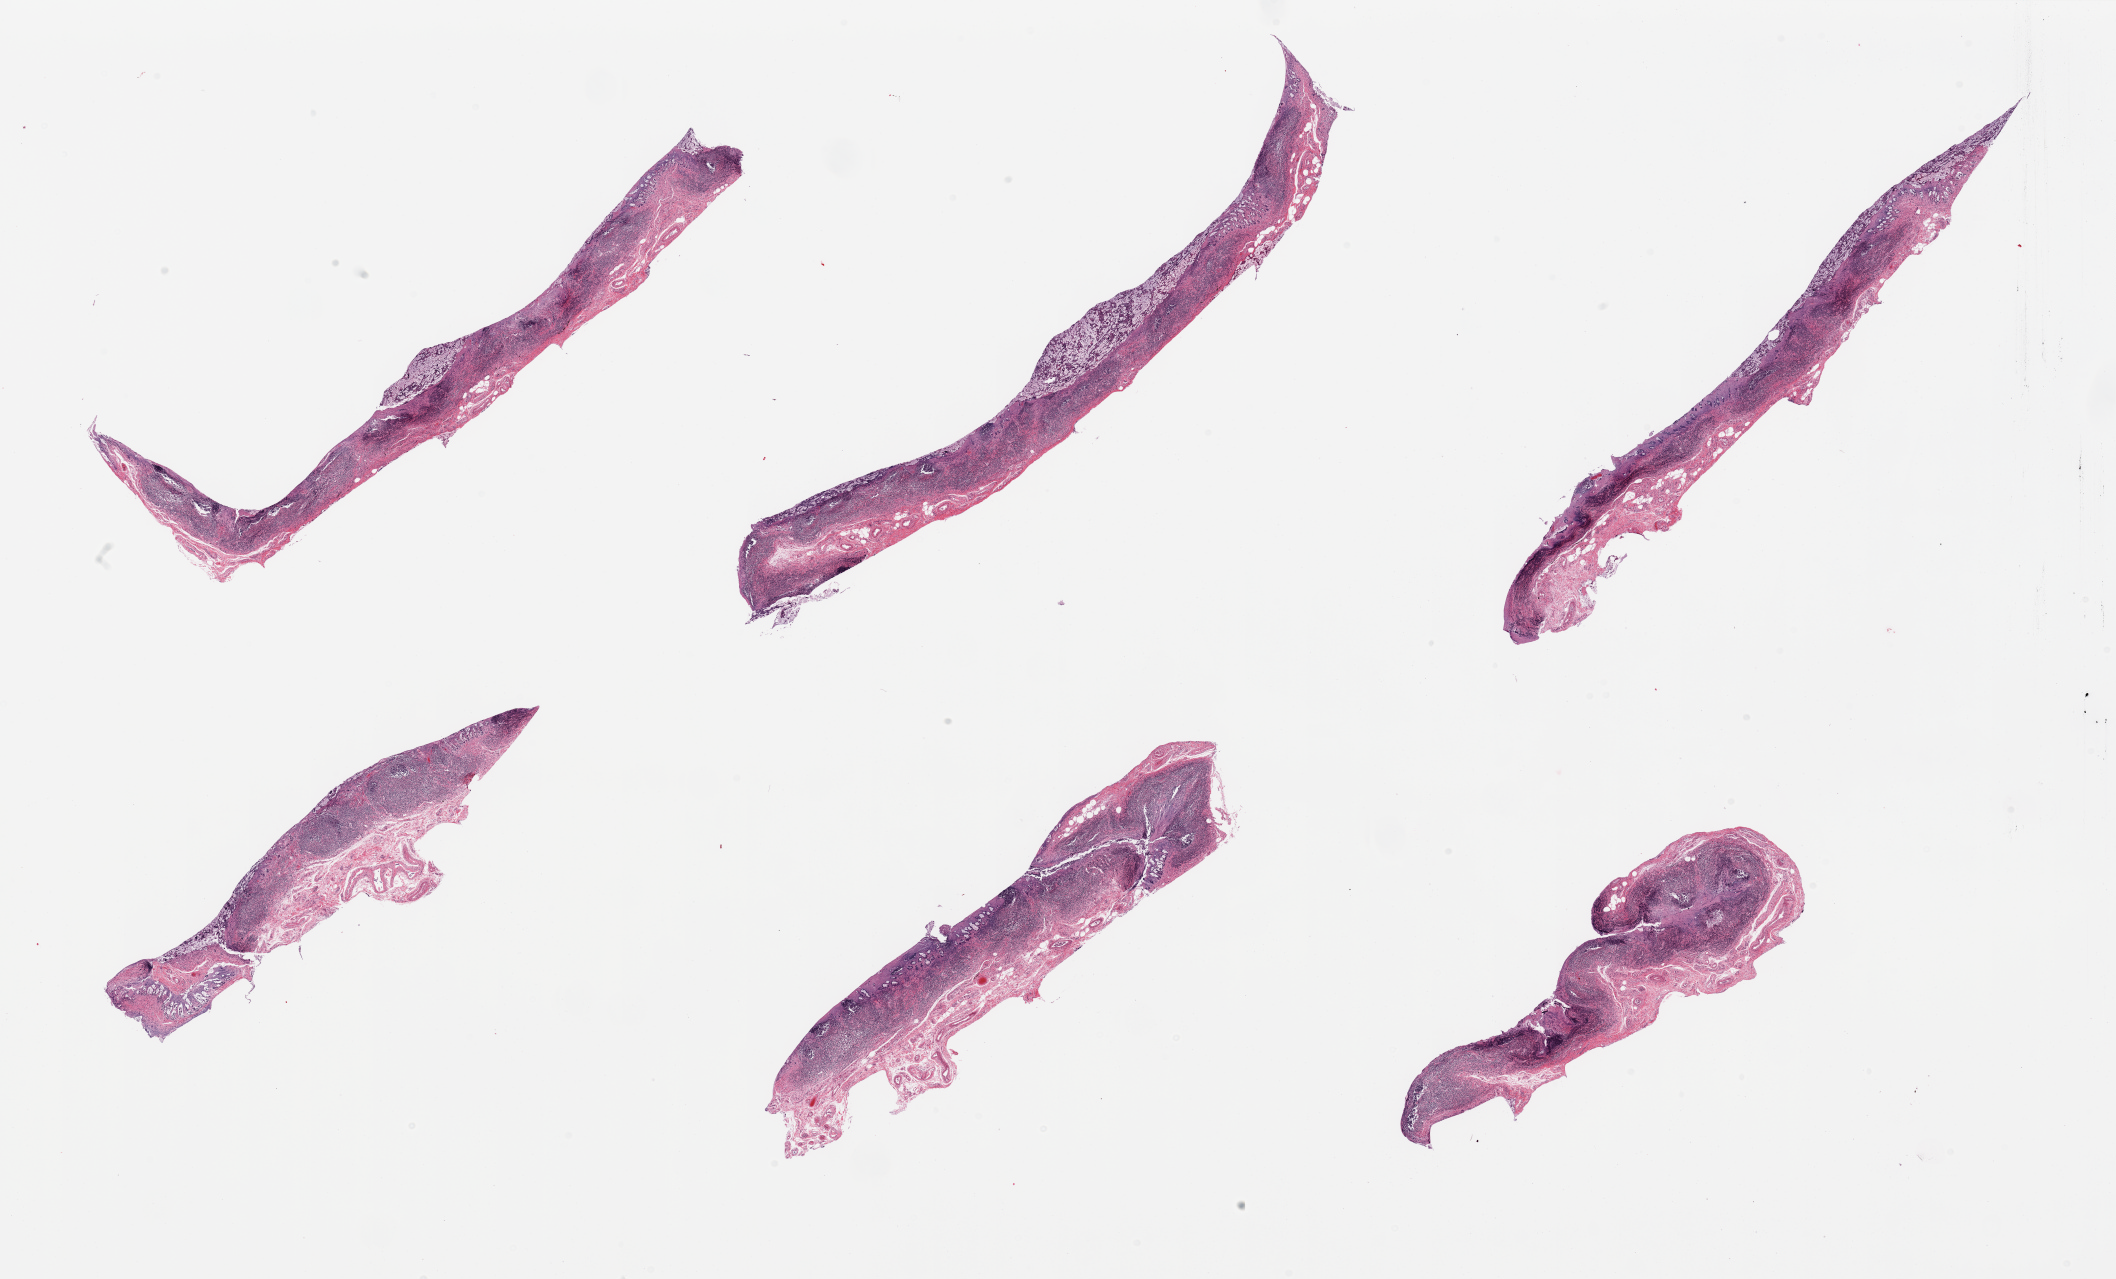
Whole-slide image, H&E stain, whole scanned area (about 33.5 x 20.2 mm, acquisition: 20x scan) shown as a low-resolution overview, PAXgene-fixed paraffin-embedded (PFPE) section, target tissue: ileum, donor tissue sample. Donor sex: male.
- pathologist's review note for this sample: 6 pieces, epithelial component completely autolyzed, abundant lymphoid elements present